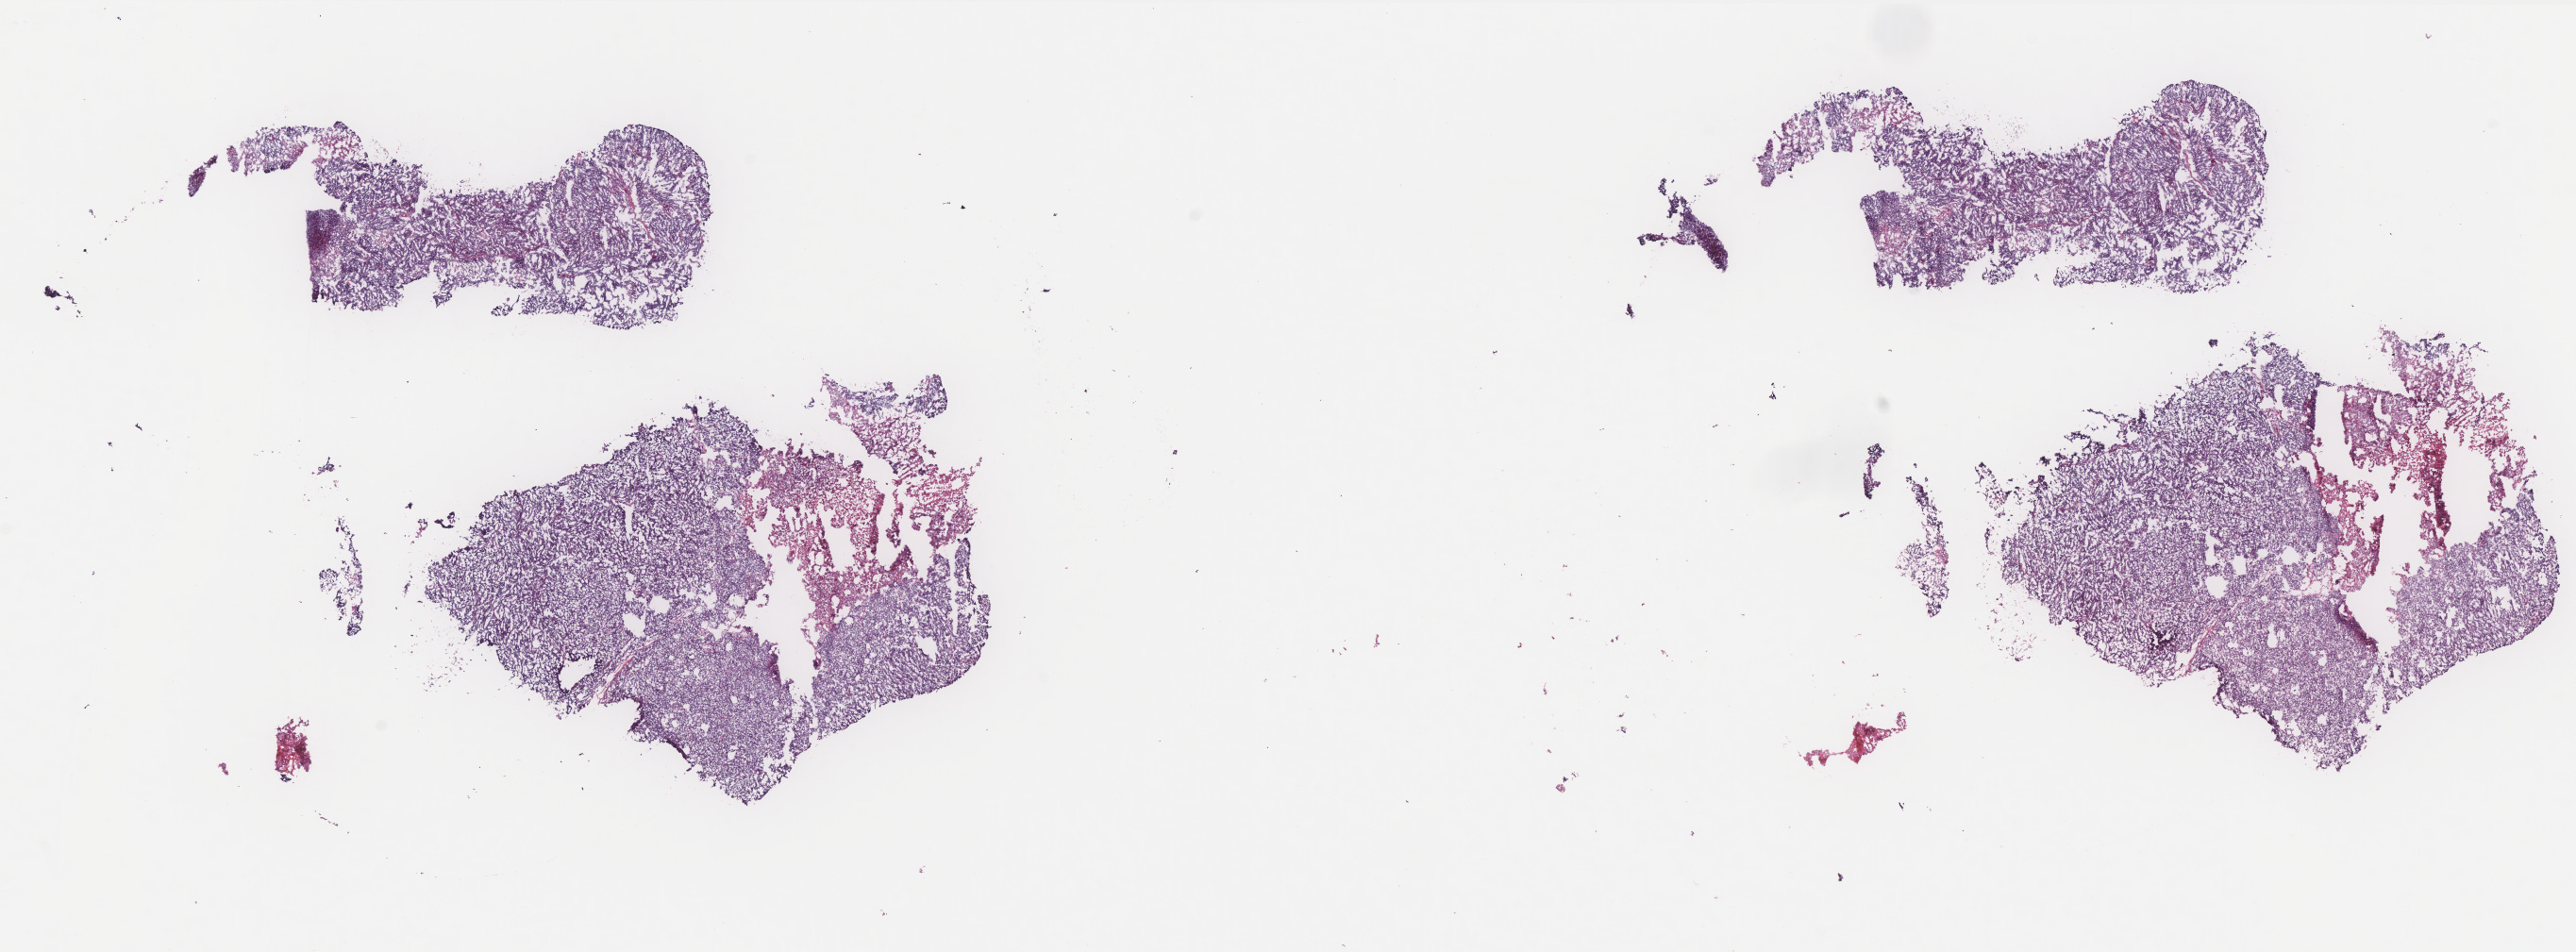
Whole-slide histology image, H&E, a low-resolution overview of the entire scanned area, about 21.9 x 8.1 mm (slide scanned at 40x), frozen section from the bottom of the tissue portion, primary tumour sample from the breast. Female, age 35 years at initial diagnosis.
Pathologic diagnosis: Infiltrating duct carcinoma, NOS.